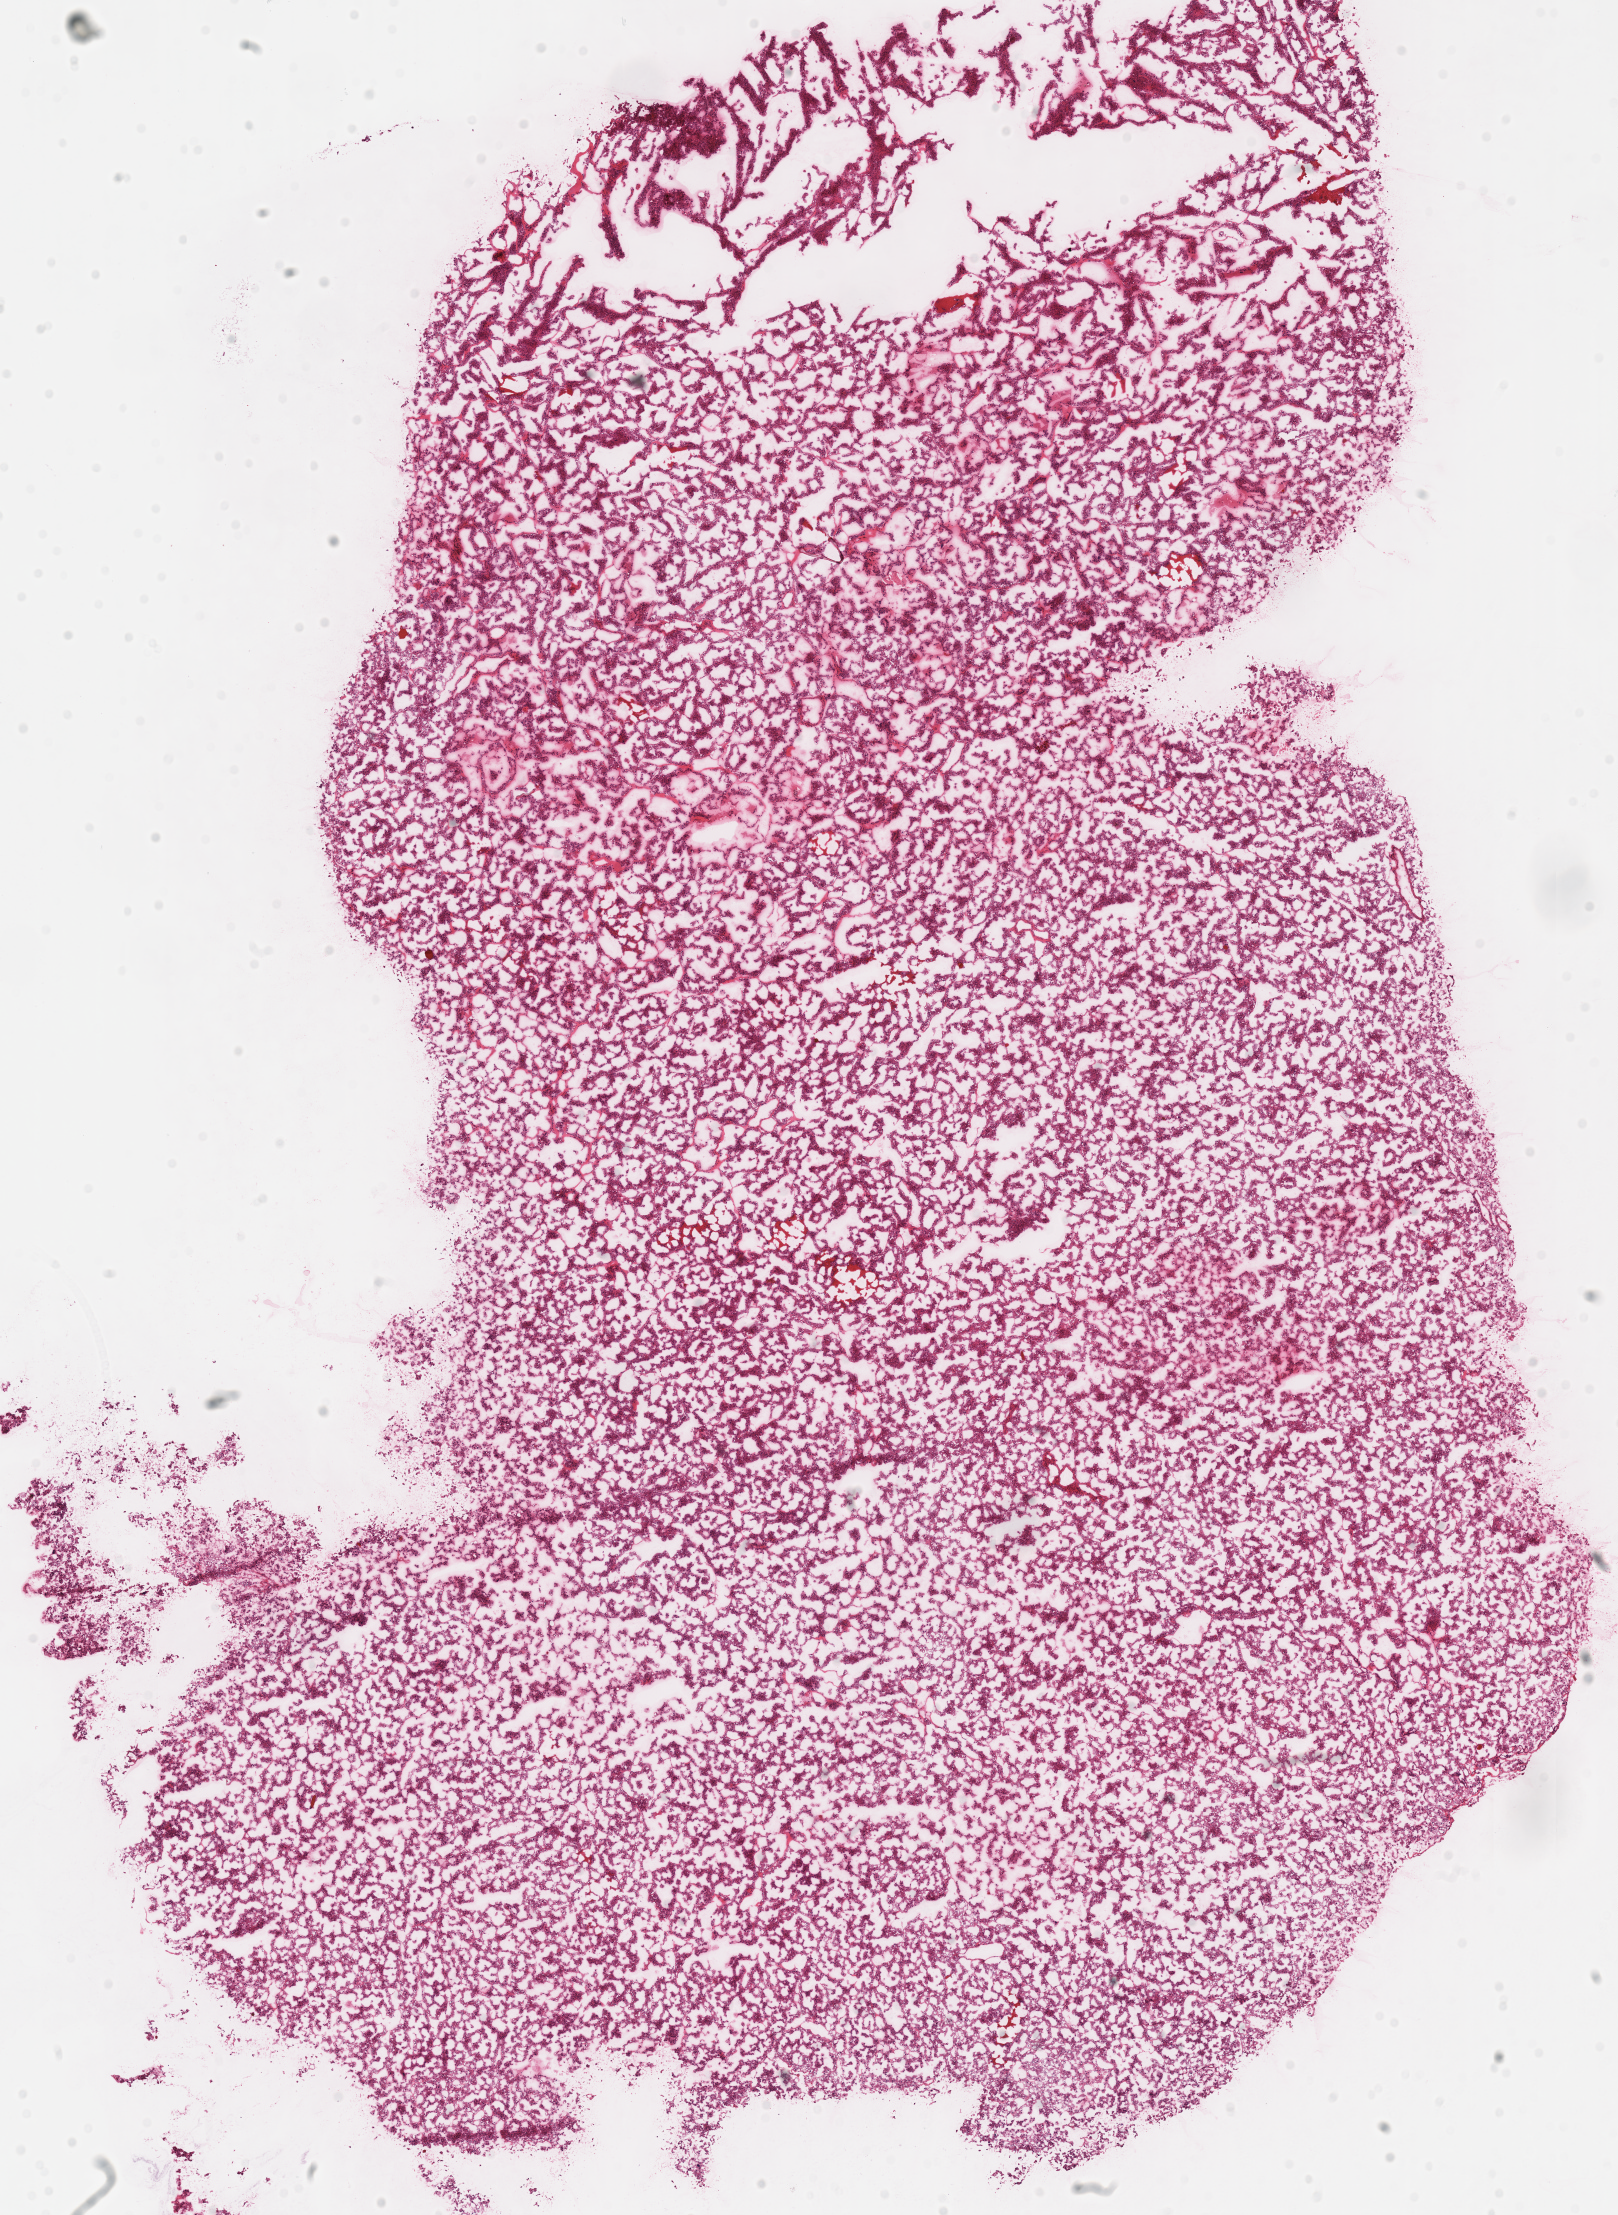
H&E-stained whole-slide image — whole scanned area (about 12.7 x 17.4 mm, from a 40x scan) shown as a low-resolution overview; frozen section from the top of the tissue portion; primary tumour sample from the kidney. Female patient; age at initial diagnosis 46 years.
Histologic diagnosis: Renal cell carcinoma, chromophobe type.